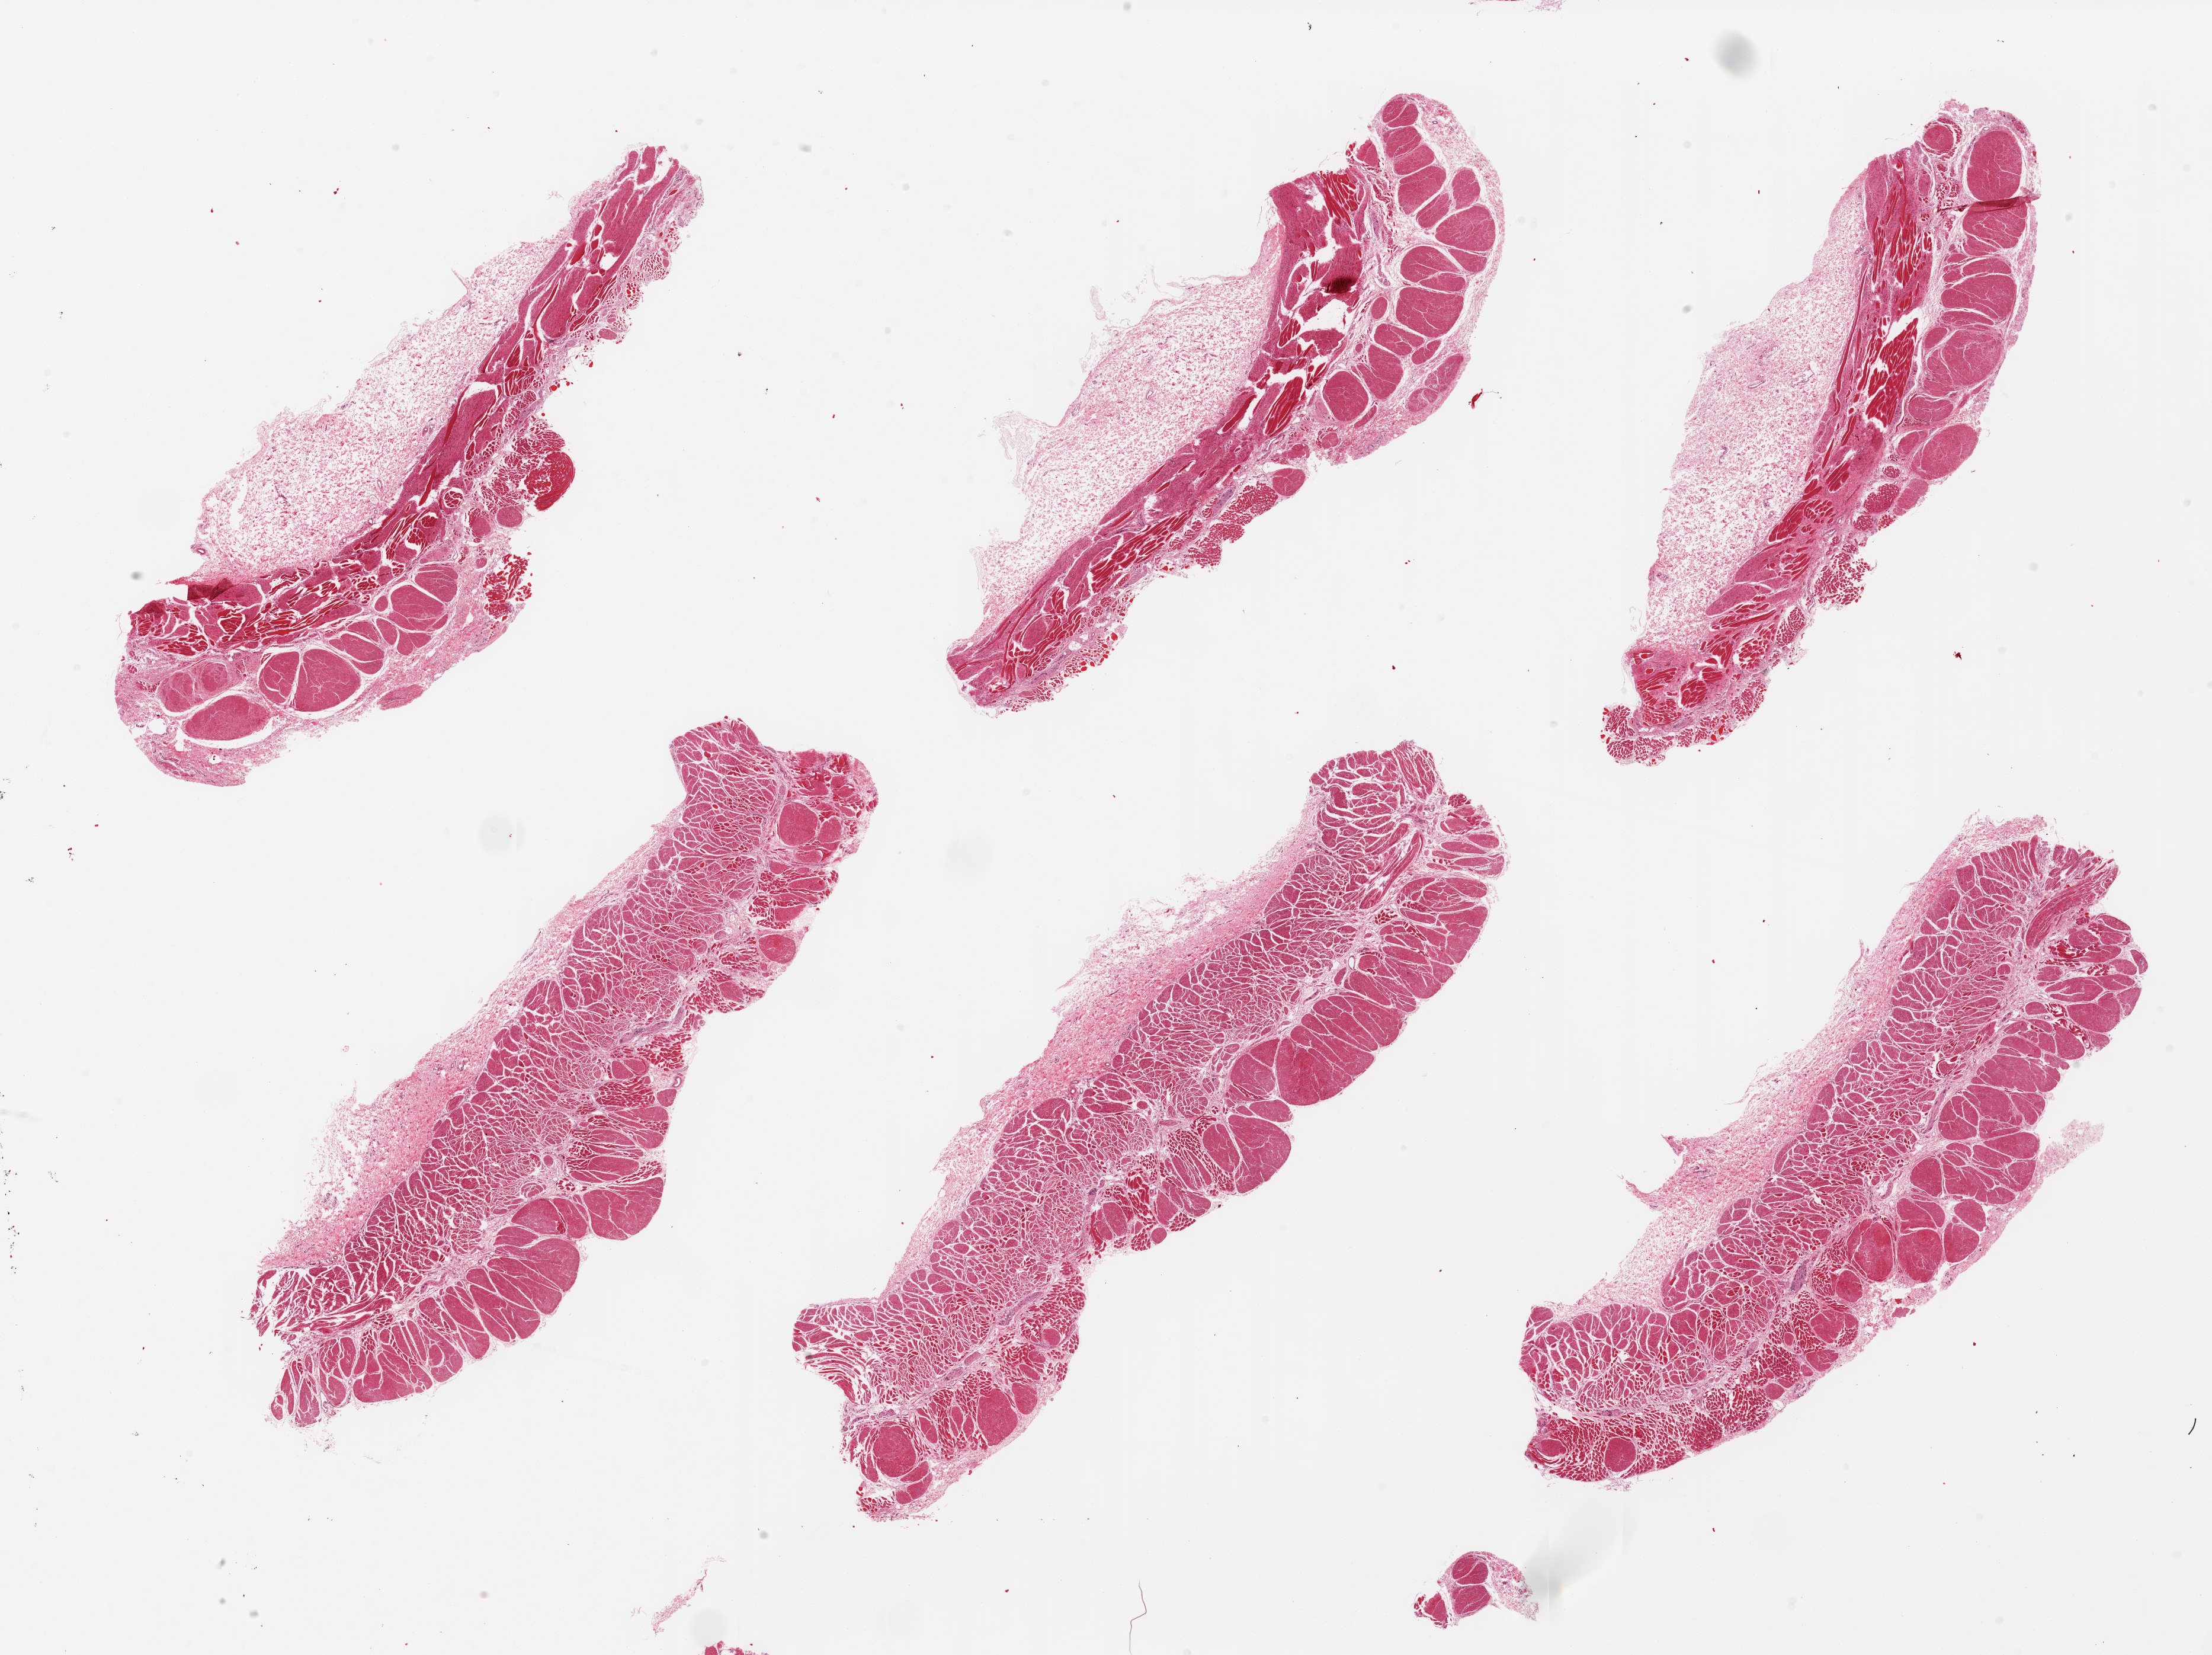
Haematoxylin and eosin whole-slide image, whole scanned area (about 29.5 x 22.1 mm) shown as a low-resolution overview. PAXgene-fixed, paraffin-embedded tissue. Sampled site (target tissue): esophageal muscle. Donor tissue sample. Donor sex: female.
Reviewer comment on this tissue sample: 6 pieces, muscularis, adherent fat layer, up to ~1mm.